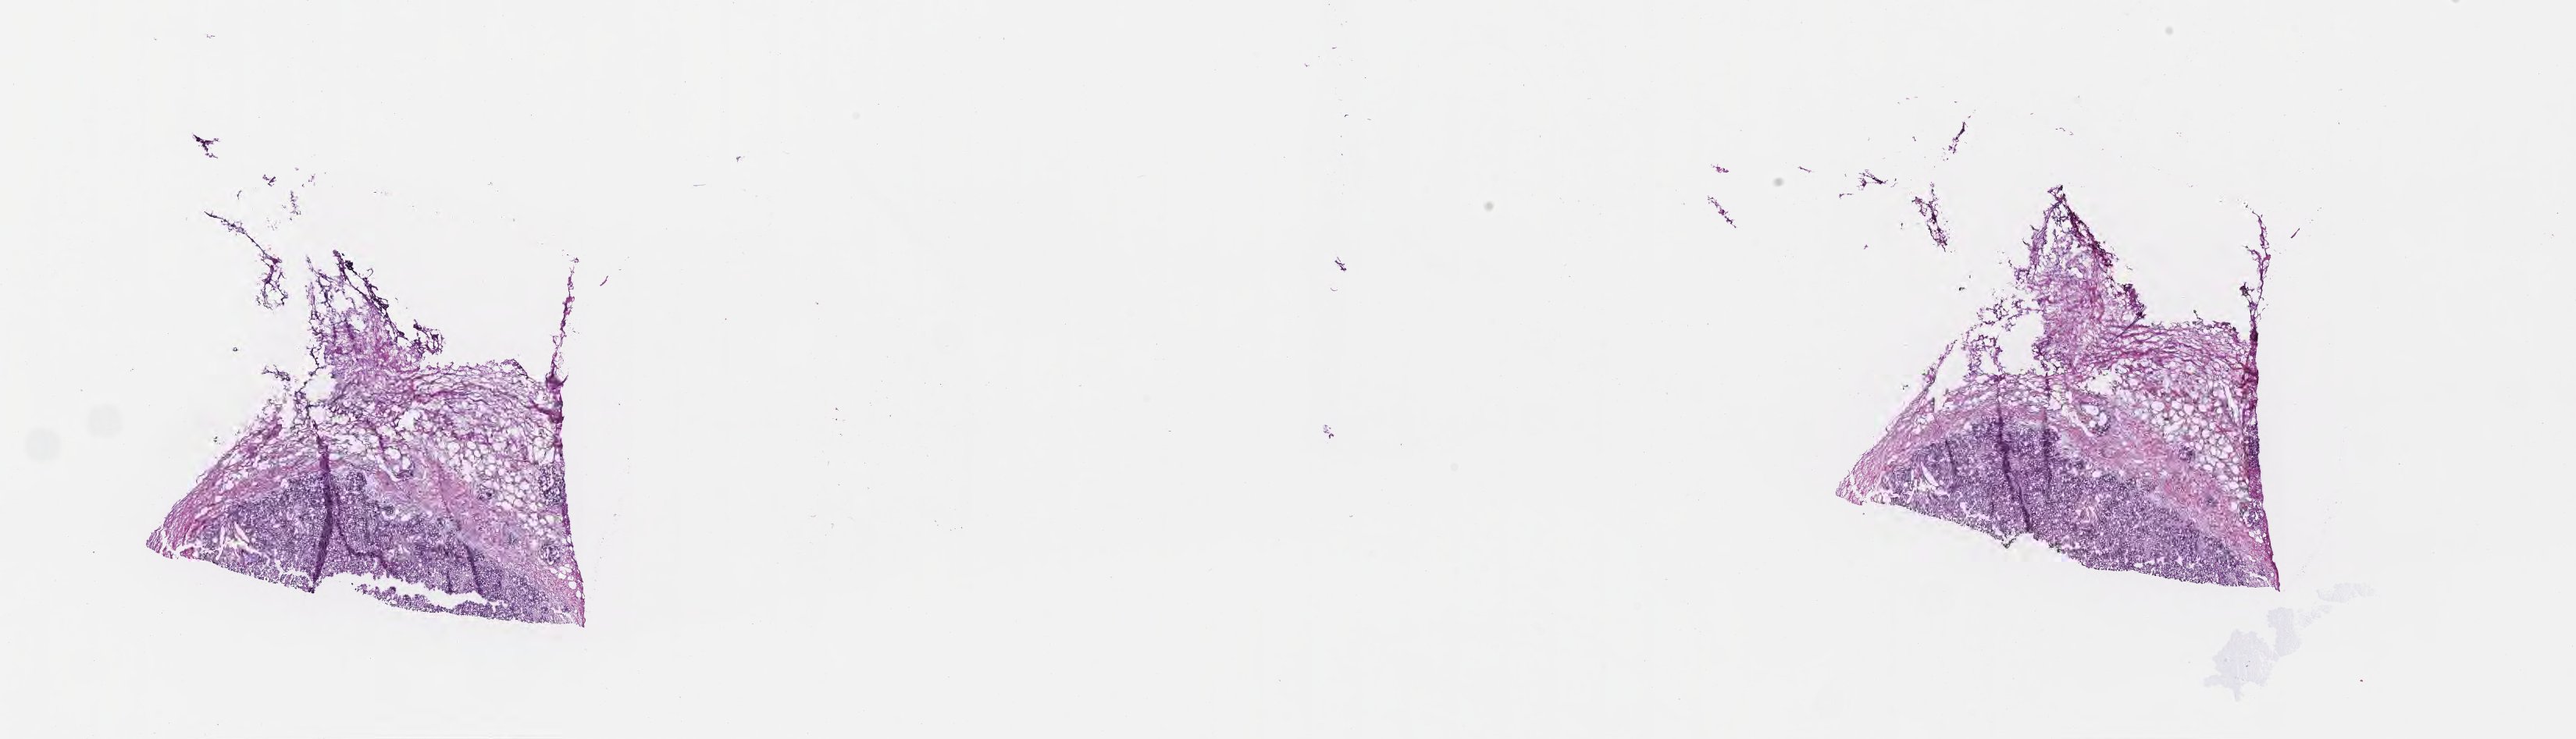
H&E whole-slide image — shown as a low-resolution overview of the whole scanned area (about 26.7 x 7.7 mm). Frozen section (tissue freezing medium). Metastatic tumor tissue, resected from lymph node. Male, age 71 years at initial diagnosis. Slide review estimates, as recorded: tumor cells 80%, tumor nuclei 80%, stromal cells 20%, necrosis 0%, normal cells 0%. Infiltration values recorded for this section: lymphocyte infiltration 6%, monocyte infiltration 2%, neutrophil infiltration 5%.
• section: top of the tissue portion
• patient diagnosis (primary): Neuroendocrine carcinoma, NOS